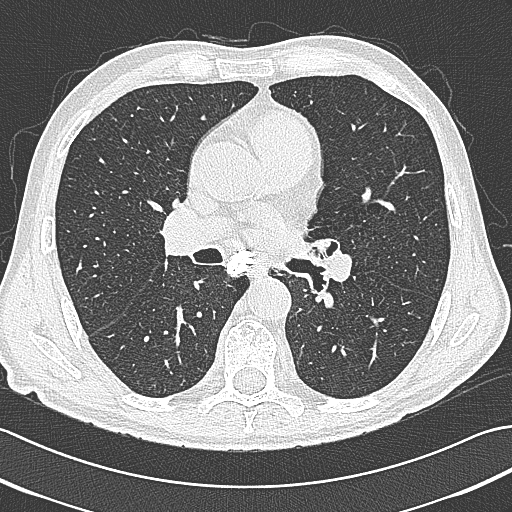
Chest CT (low-dose screening protocol), one axial image. First (baseline) screen. Lung window (W 1500 / L -600 HU). 1 mm slice thickness. Slice 176 of 380 in the series. 512 × 512 image matrix. Male participant, aged 65 years at enrolment. Current smoker at enrolment.
Lesion marked by an expert reader, bounding box [x1, y1, x2, y2] px = [304, 230, 348, 277]. No non-calcified nodule or mass ≥4 mm was recorded by the screening reader at this exam. Participant outcome: lung cancer diagnosed 161 days after this screen — large cell neuroendocrine carcinoma, left hilum, left main stem bronchus, stage IIIB (AJCC 6th edition), 70 mm at pathology.